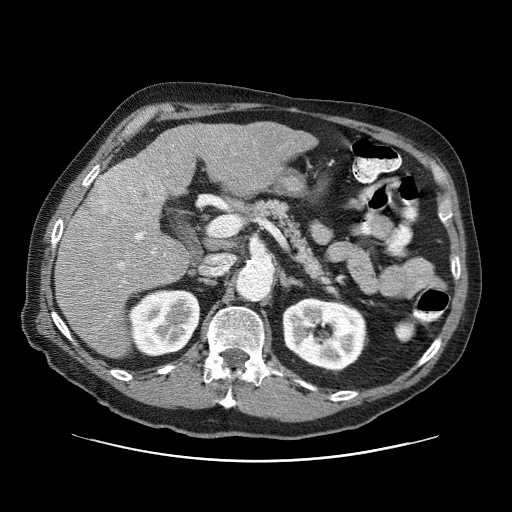
Contrast-enhanced abdominal CT (liver protocol), one axial slice. Reconstruction kernel STANDARD. 120 kVp. One of 3 acquisitions stored at this slice position. Soft-tissue window (W 400 / L 40 HU). 2.5 mm slice thickness. 512 × 512 image matrix. From the clinical record (not read from this slice): diagnosis: hepatocellular carcinoma (patient treated with transarterial chemoembolisation; whether this scan precedes or follows treatment is not stated here); TNM stage (as recorded): Stage-IIIA; Child-Pugh class: A; tumour differentiation: well differentiated; tumour nodularity: multinodular.
Outlined on this slice (semi-automatic segmentation, software-assisted and operator-edited):
- liver parenchyma outside the tumour (the mass and vessels are separate outlines, so this box may not span the whole liver): box from (x=54, y=122) to (x=317, y=358) px
- mass: (x=88, y=160)–(x=165, y=227)
- liver vessels: (x=118, y=232)–(x=166, y=283)